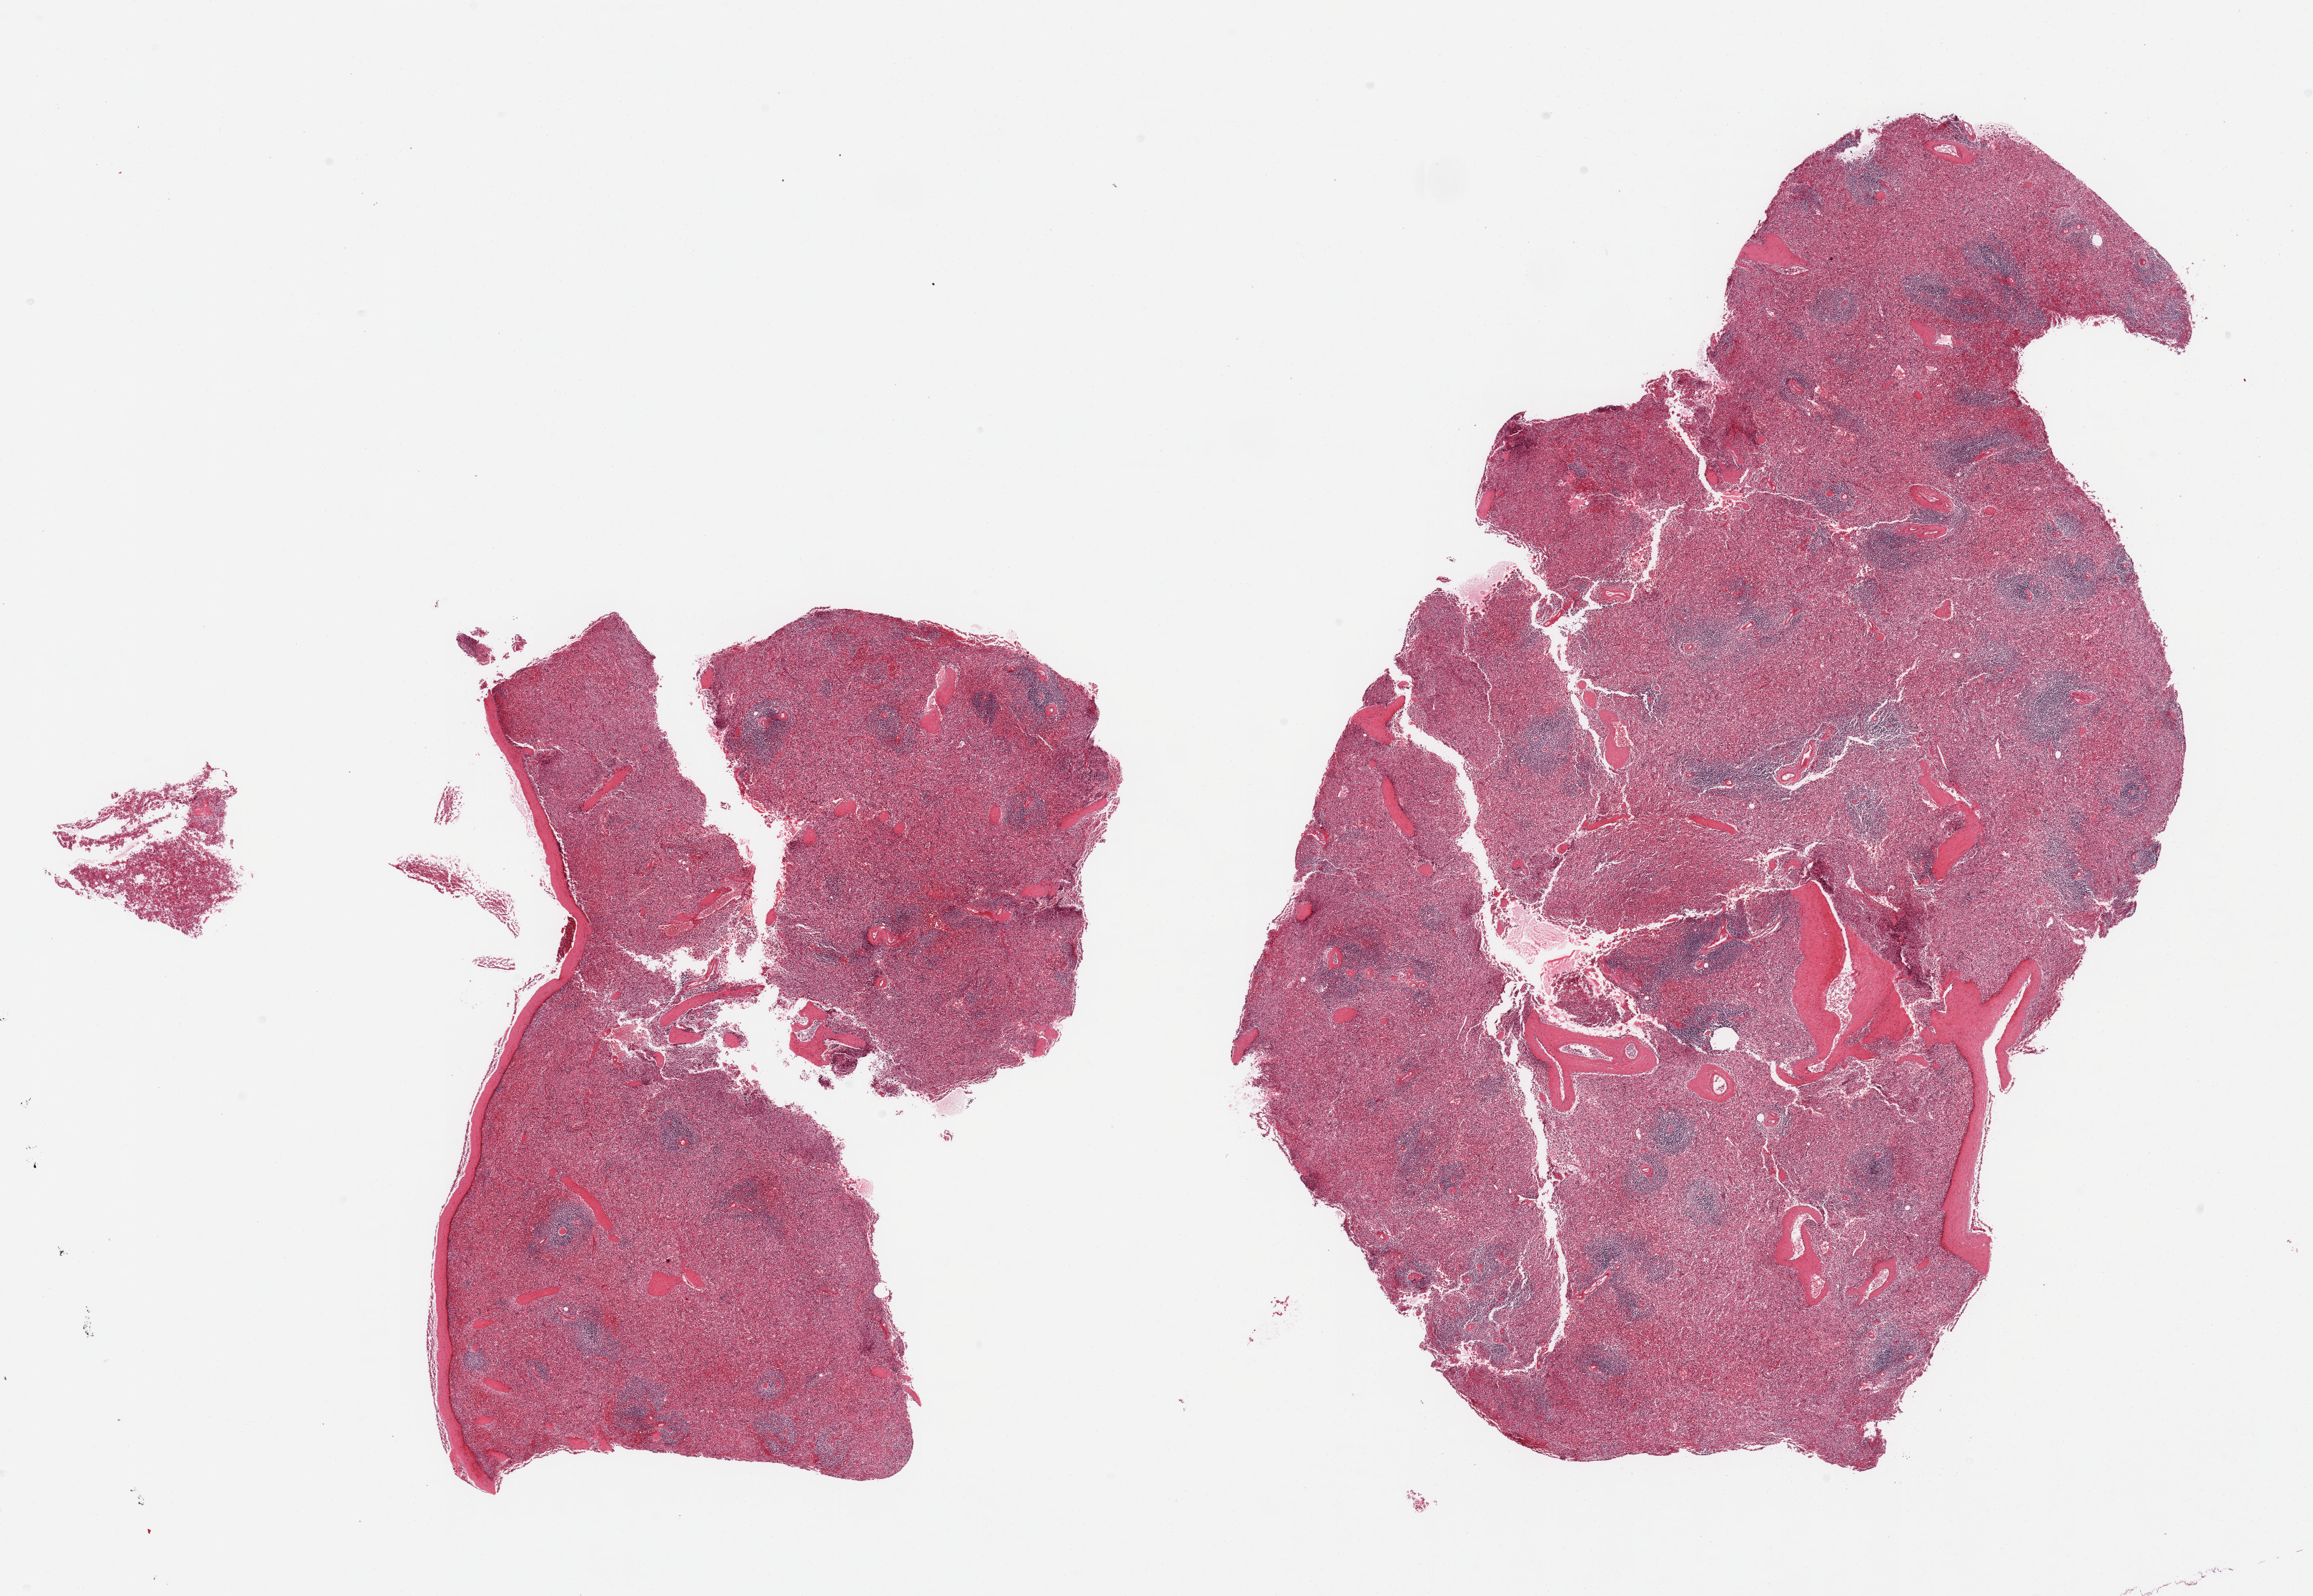
H&E whole-slide image, whole scanned area (about 25.6 x 17.7 mm, slide scanned at 20x) shown as a low-resolution overview; PAXgene-fixed, paraffin-embedded tissue; sampled site (target tissue): spleen; donor tissue sample. Donor sex: female.
- reviewer comment on this tissue sample: 2 pieces; congested and fragmented